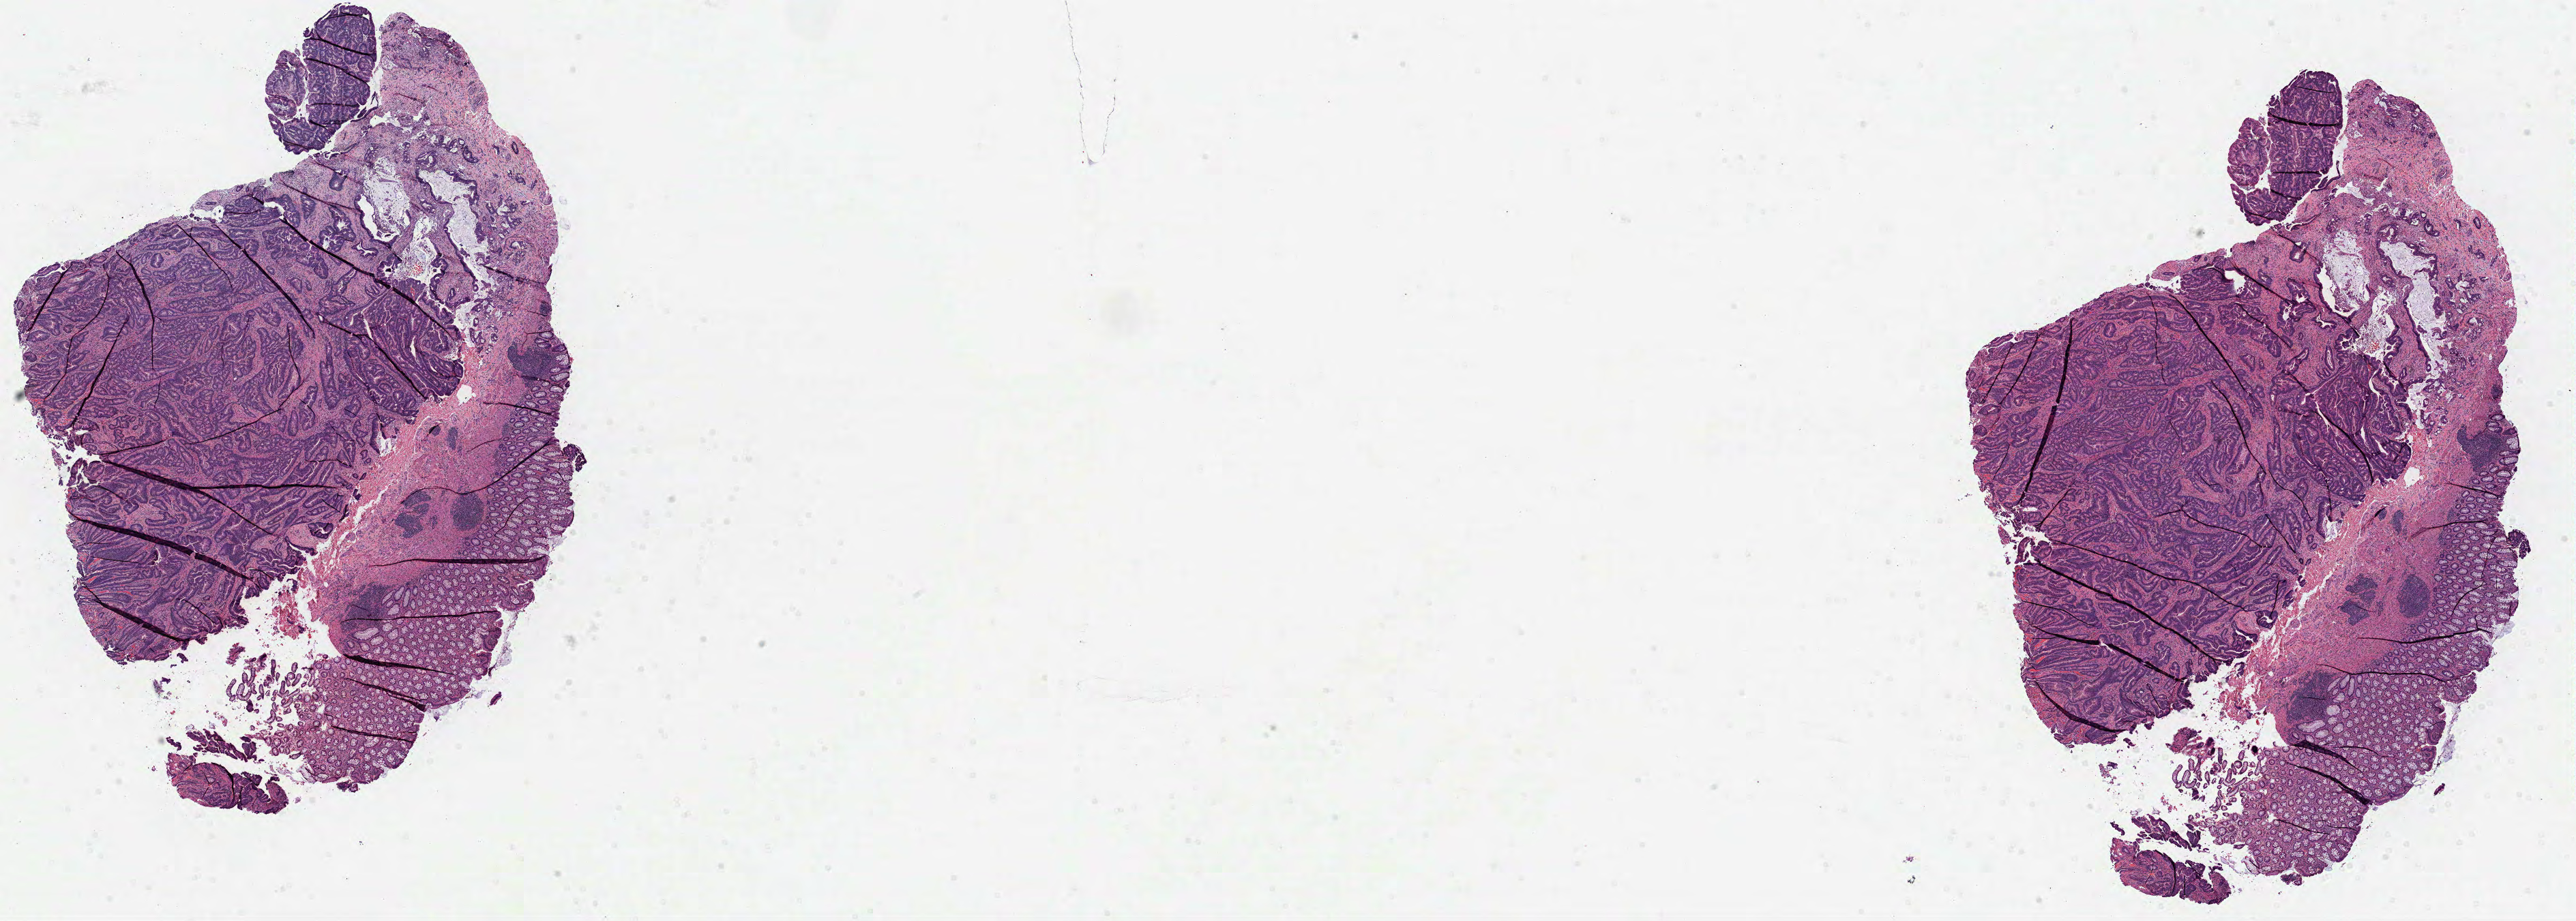
H&E whole-slide image — a low-resolution overview of the entire scanned area, about 30.5 x 10.9 mm. Formalin-fixed paraffin-embedded (FFPE) diagnostic section. Rectum, primary tumour sample. Female, age 72 years at initial diagnosis.
TNM: T3 N1b MX. Lymph nodes positive (case pathology): 2 of 52 examined. AJCC pathologic stage: IIIB (7th edition). Pathologic diagnosis: Adenocarcinoma, NOS (rectosigmoid junction).